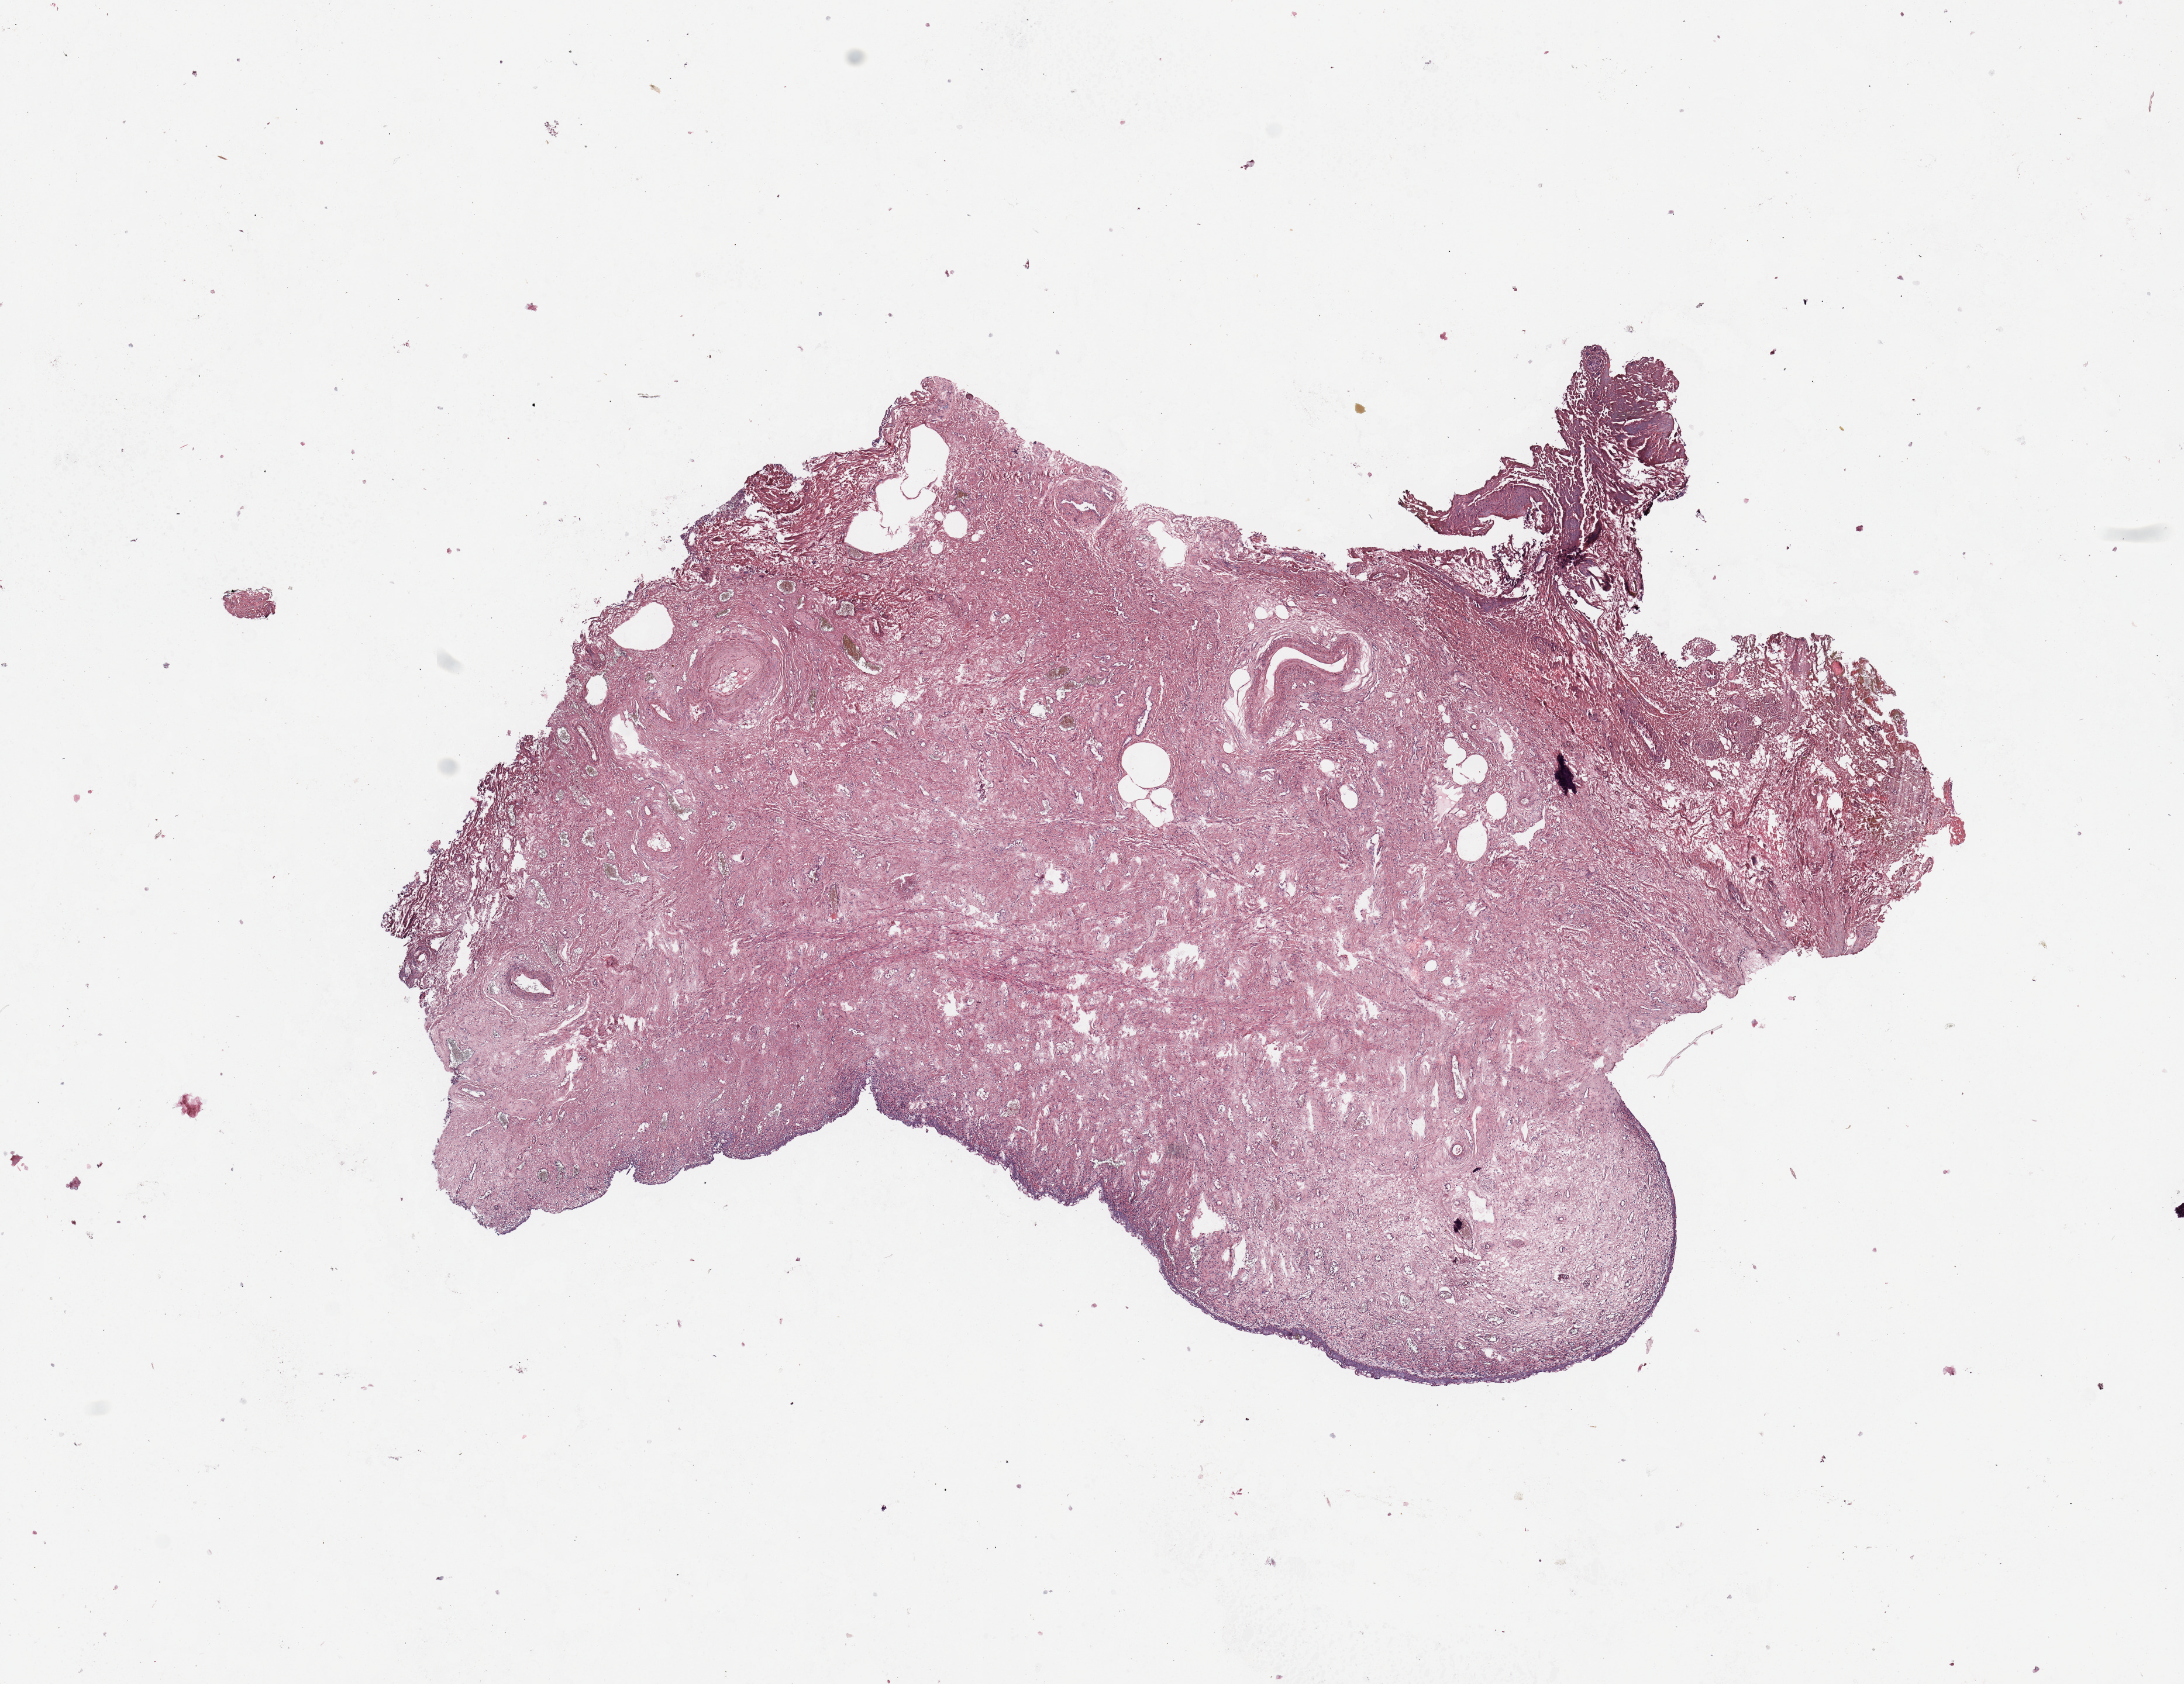
Digitized Hematoxylin and eosin (H&E) stained tissue section (whole slide), shown as a low-resolution overview of the whole scanned area (about 14.8 x 11.4 mm), uterus, normal (non-tumour) tissue. Female, 55 y/o.
• this section: normal (non-tumour) tissue from the same patient
• patient diagnosis: Endometrioid adenocarcinoma, NOS